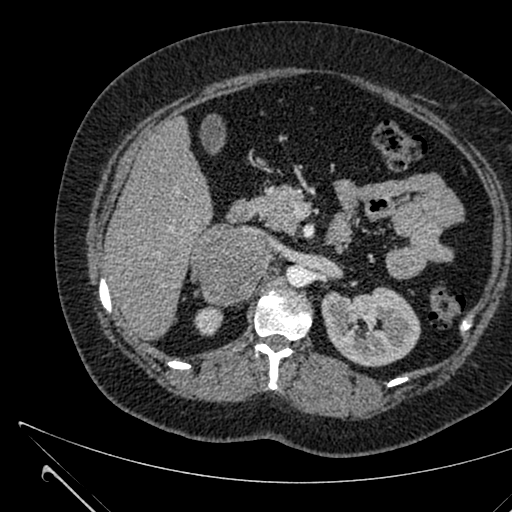
Contrast-enhanced abdominal CT, one axial slice; position 388 of 731 along the scan axis; 120 kVp; intravenous contrast given; soft-tissue window (W 400 / L 40 HU); 512 × 512 image matrix, field of view 376 × 376 mm. Patient: female, 36 years. From the clinical record (not read from this slice): diagnosis: adrenocortical carcinoma; tumour side: right adrenal; tumour size at pathology: 10 cm; Ki-67 index: 20 %; stage (as recorded): 4.
Outlined on this slice (semi-automatic segmentation, software-assisted and operator-edited):
- mass: box from (x=193, y=226) to (x=268, y=305) px